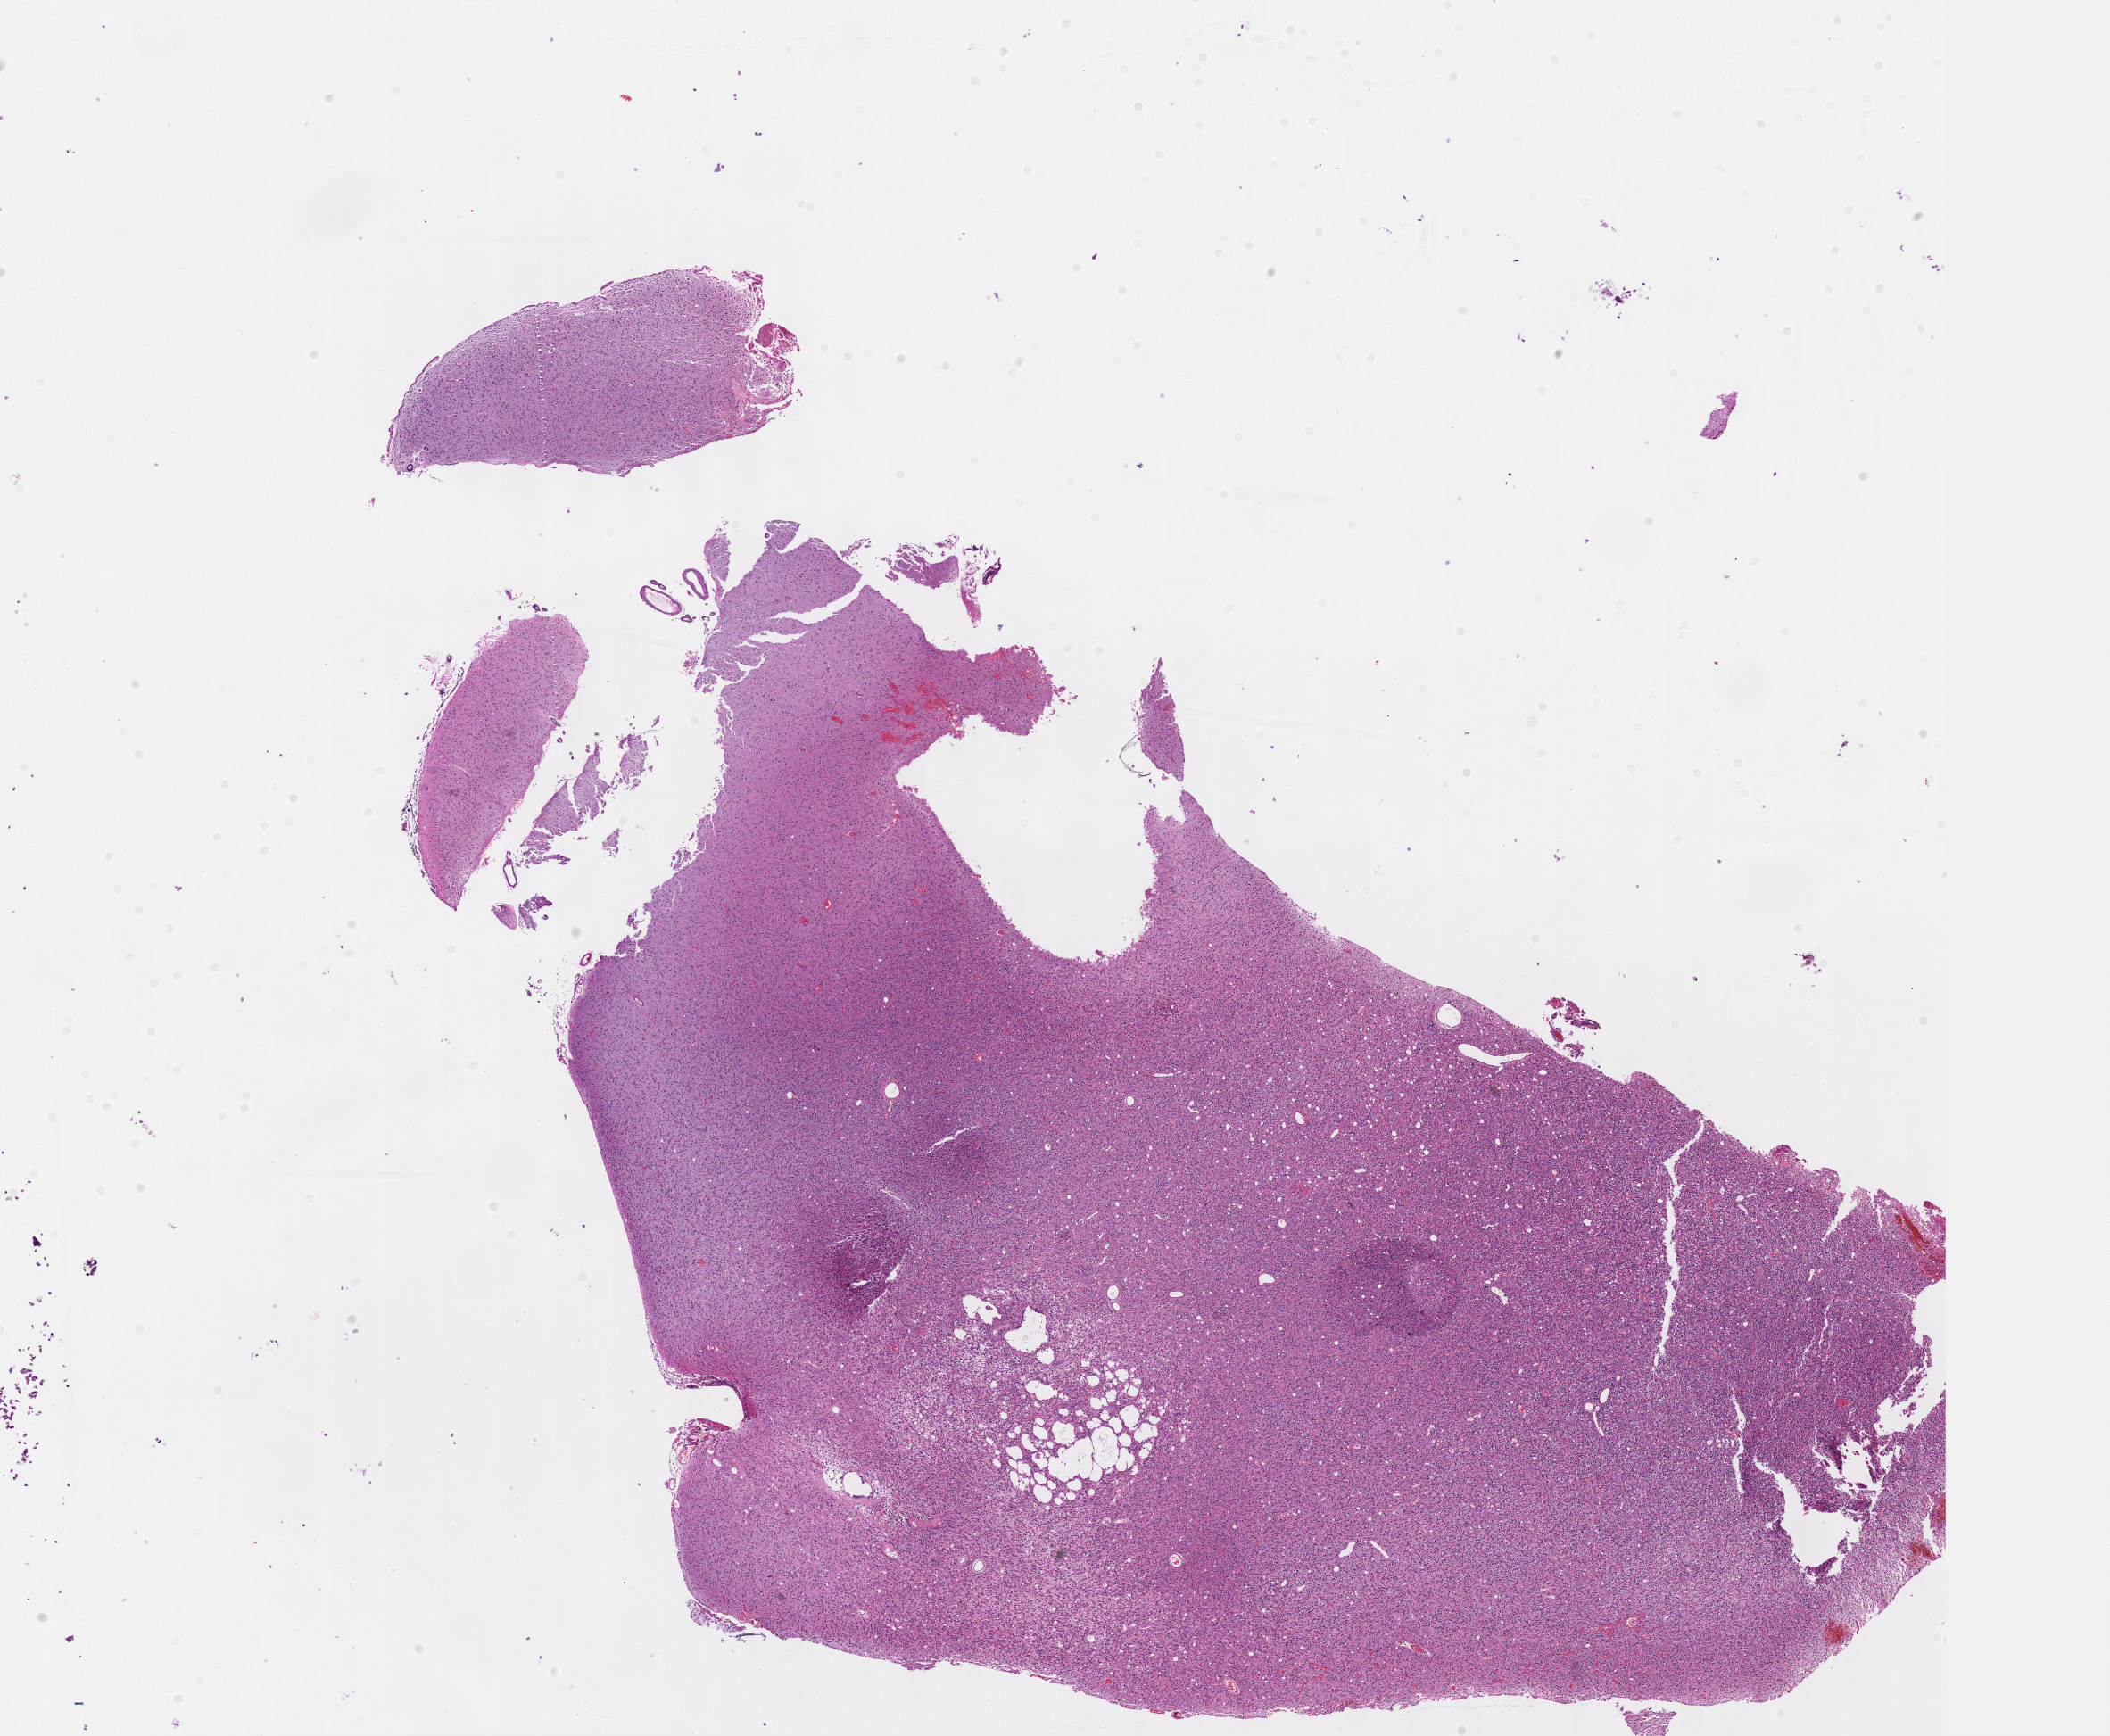
H&E whole-slide image — whole scanned area (about 19.1 x 15.7 mm, acquisition: 40x scan) shown as a low-resolution overview; formalin-fixed paraffin-embedded (FFPE) diagnostic section; sample: recurrent tumour, brain. Female patient; age at initial diagnosis 41 years.
* this section: recurrent tumour
* patient diagnosis: Astrocytoma, NOS (cerebrum)